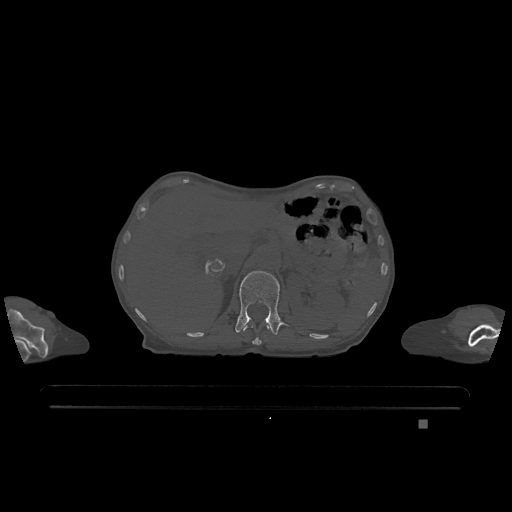
CT including the spine, one axial slice; position 488 of 1317 along the scan axis; bone window (W 1800 / L 400 HU); 512 × 512 image matrix. Female patient, age 74 years. Case-level facts recorded for this patient, not image findings: primary cancer: lung.
Annotated regions visible in this slice (semi-automatically segmented with operator editing):
- L1 vertebra: bounding box [x1, y1, x2, y2] px = [235, 271, 285, 335]
- T12 vertebra: [243, 326, 269, 345]